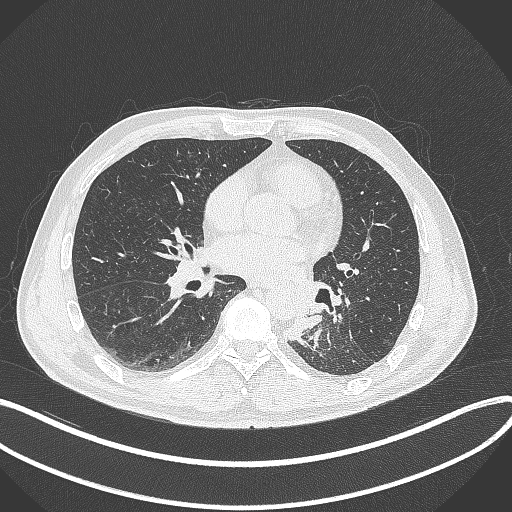
Chest CT, one axial slice. Position 148 of 329 along the scan axis. 120 kVp. Lung window (W 1500 / L -600 HU). 512 × 512 image matrix. Patient: male, 59 years. From the clinical record (not read from this slice): clinical TNM (as recorded): T2a N2 M0.
Structures marked on this image (rectangle marked by the reading radiologist):
- lung tumour (recorded histology: squamous cell carcinoma): bounding box <281,305,328,346> (left, top, right, bottom; pixels)